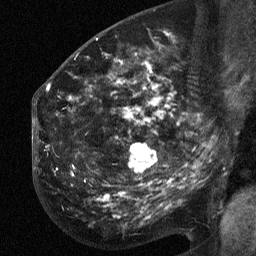
Breast MRI (dynamic contrast-enhanced), one sagittal slice. Position 33 of 64 along the scan axis. Dynamic contrast-enhanced study with each time point stored as its own series, time point 2 of 3 at this slice position (early post-contrast, ordered by acquisition time). 1.5 T. TE 4.8 ms, TR 27 ms. 2.3 mm slice thickness. 256 × 256 image matrix, field of view 200 × 200 mm. Patient: female, 50 years. From the clinical record (not read from this slice): setting: breast cancer imaged before/during neoadjuvant chemotherapy; receptor status: HER2-positive.
Structures marked on this image (semi-automatically segmented with operator editing):
- analysis volume of interest (the breast-tissue region the enhancement analysis was run in; not a lesion): box from (x=53, y=64) to (x=211, y=213) px
- tumour enhancement mask (voxels above the 90 % enhancement threshold inside the analysis volume of interest): (x=131, y=144)–(x=155, y=170)